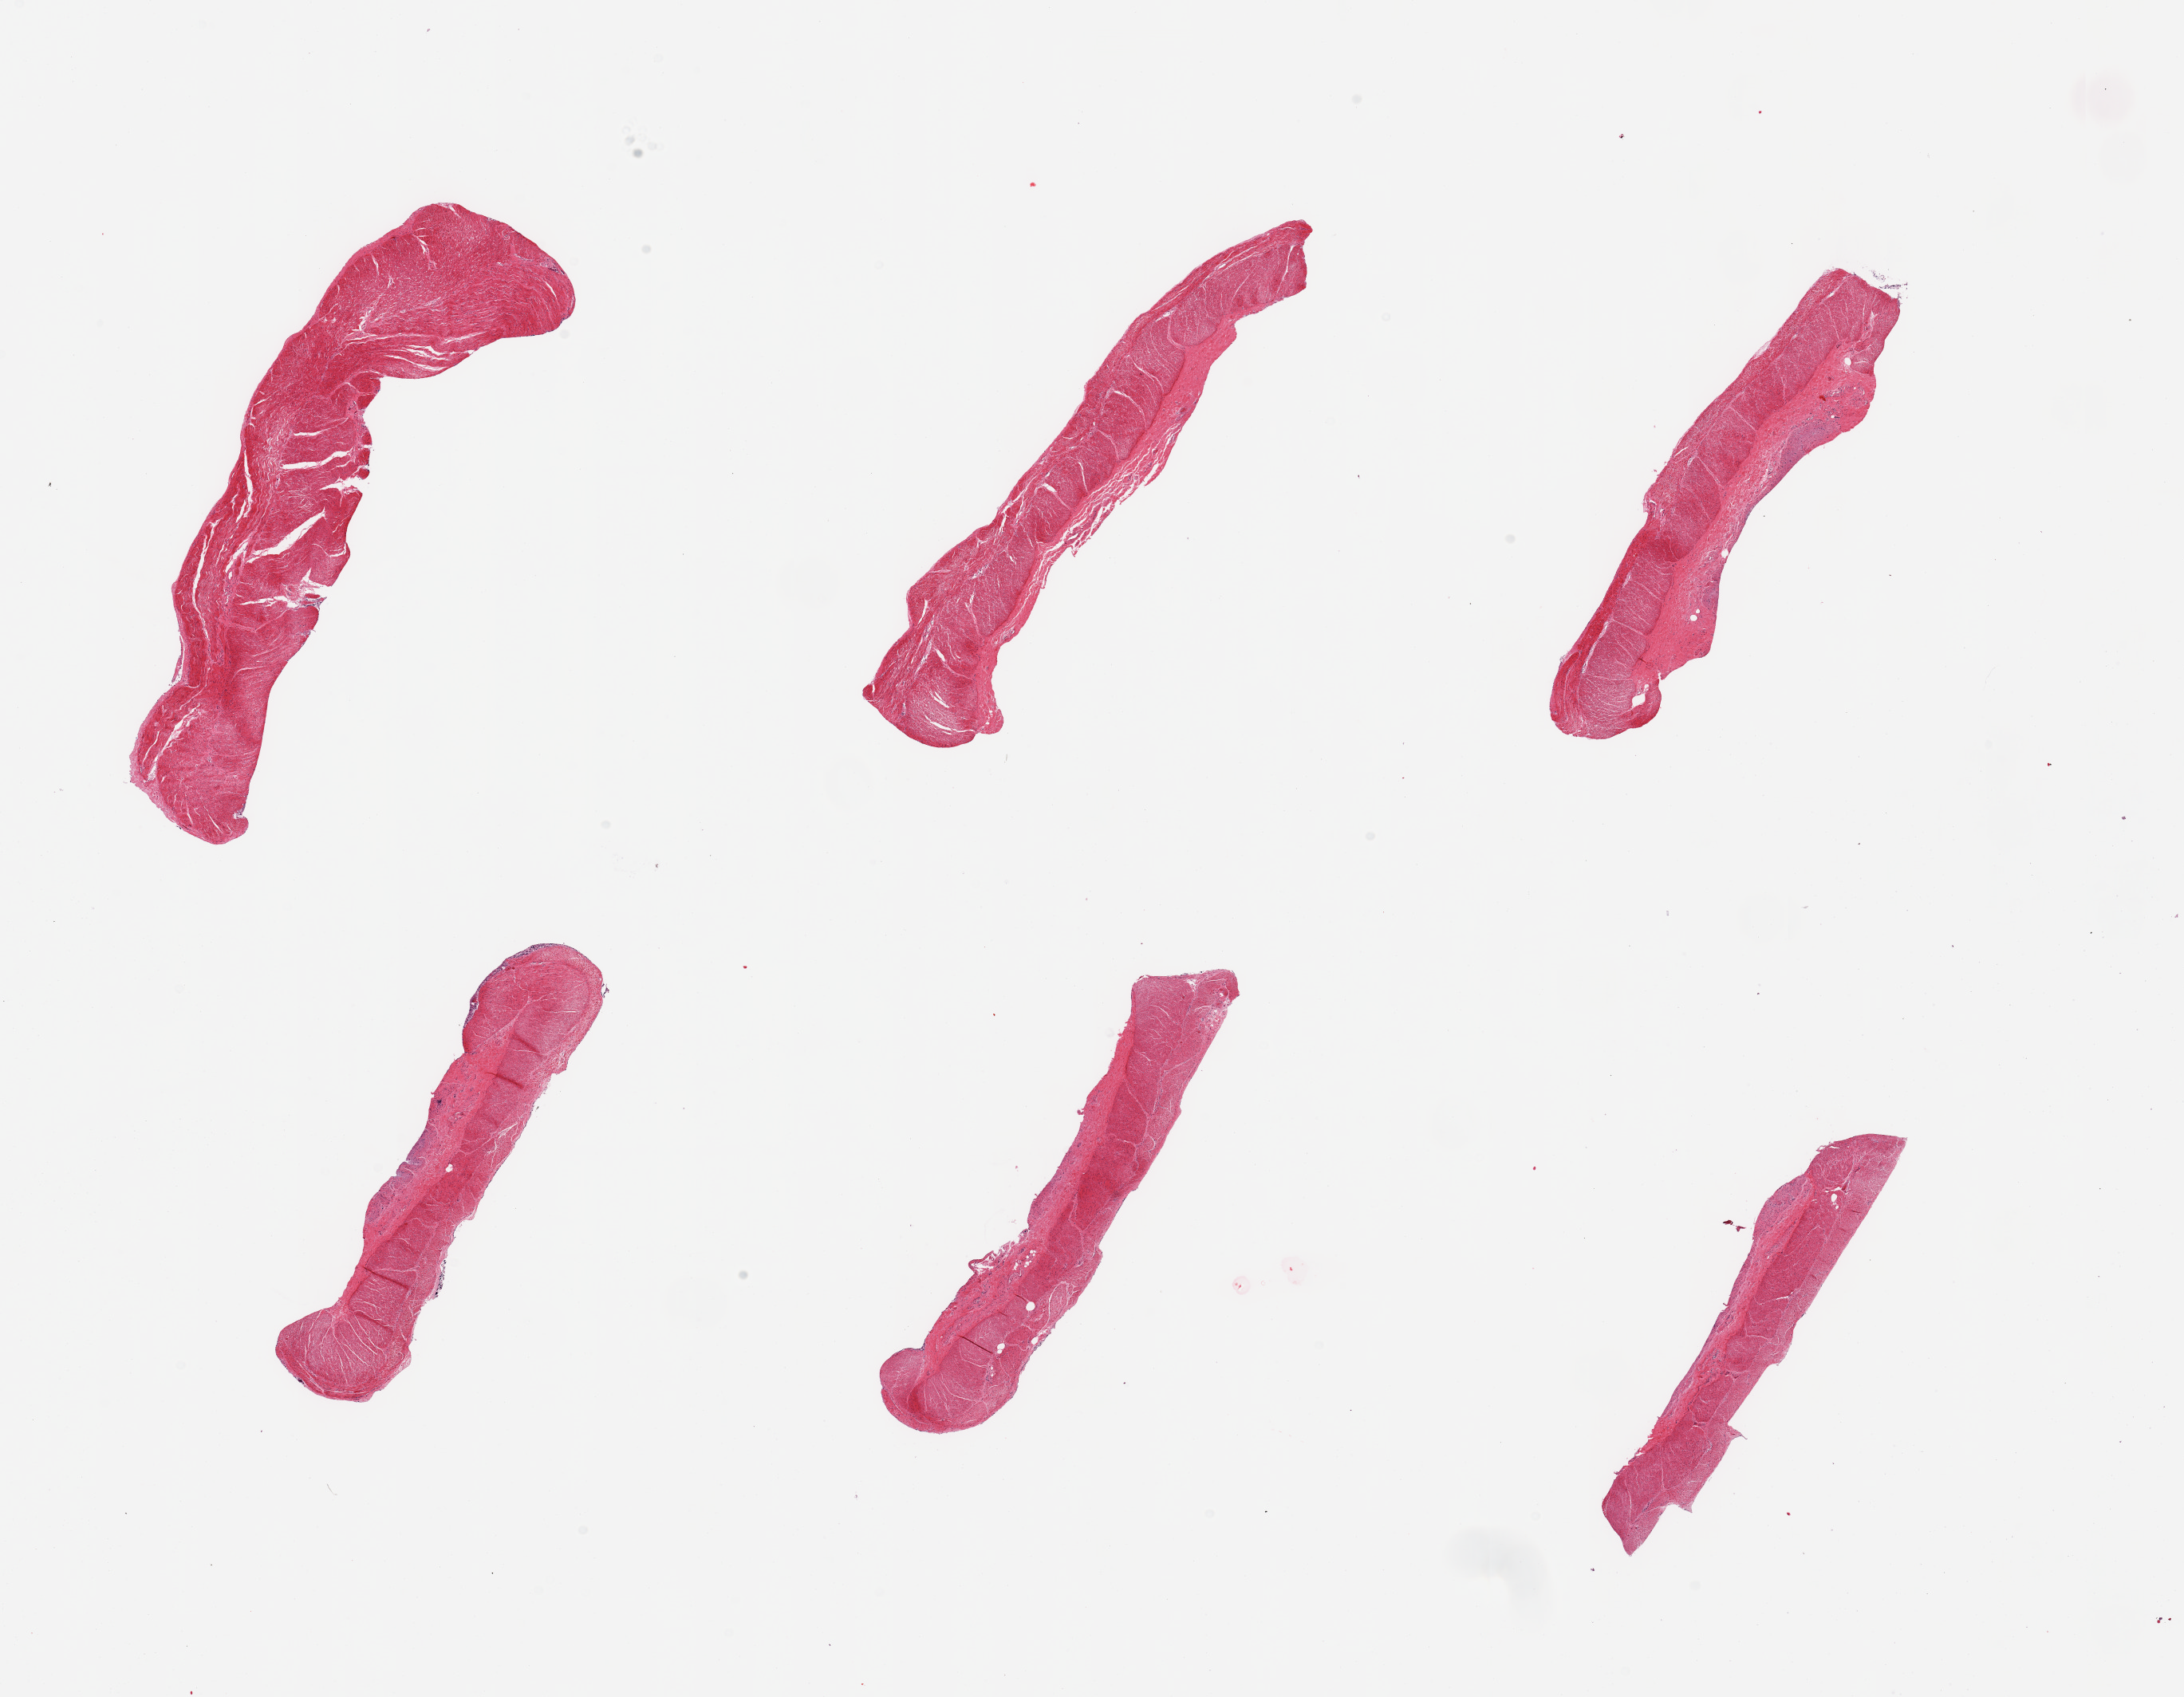
Digitized H&E-stained section, low-resolution overview of the scanned area, about 21.7 x 16.8 mm (from a 20x scan), PAXgene-fixed paraffin-embedded (PFPE) section, sampled site (target tissue): sigmoid colon, tissue donor sample. Female donor.
Review note (as recorded): 6 pieces; well trimmed.